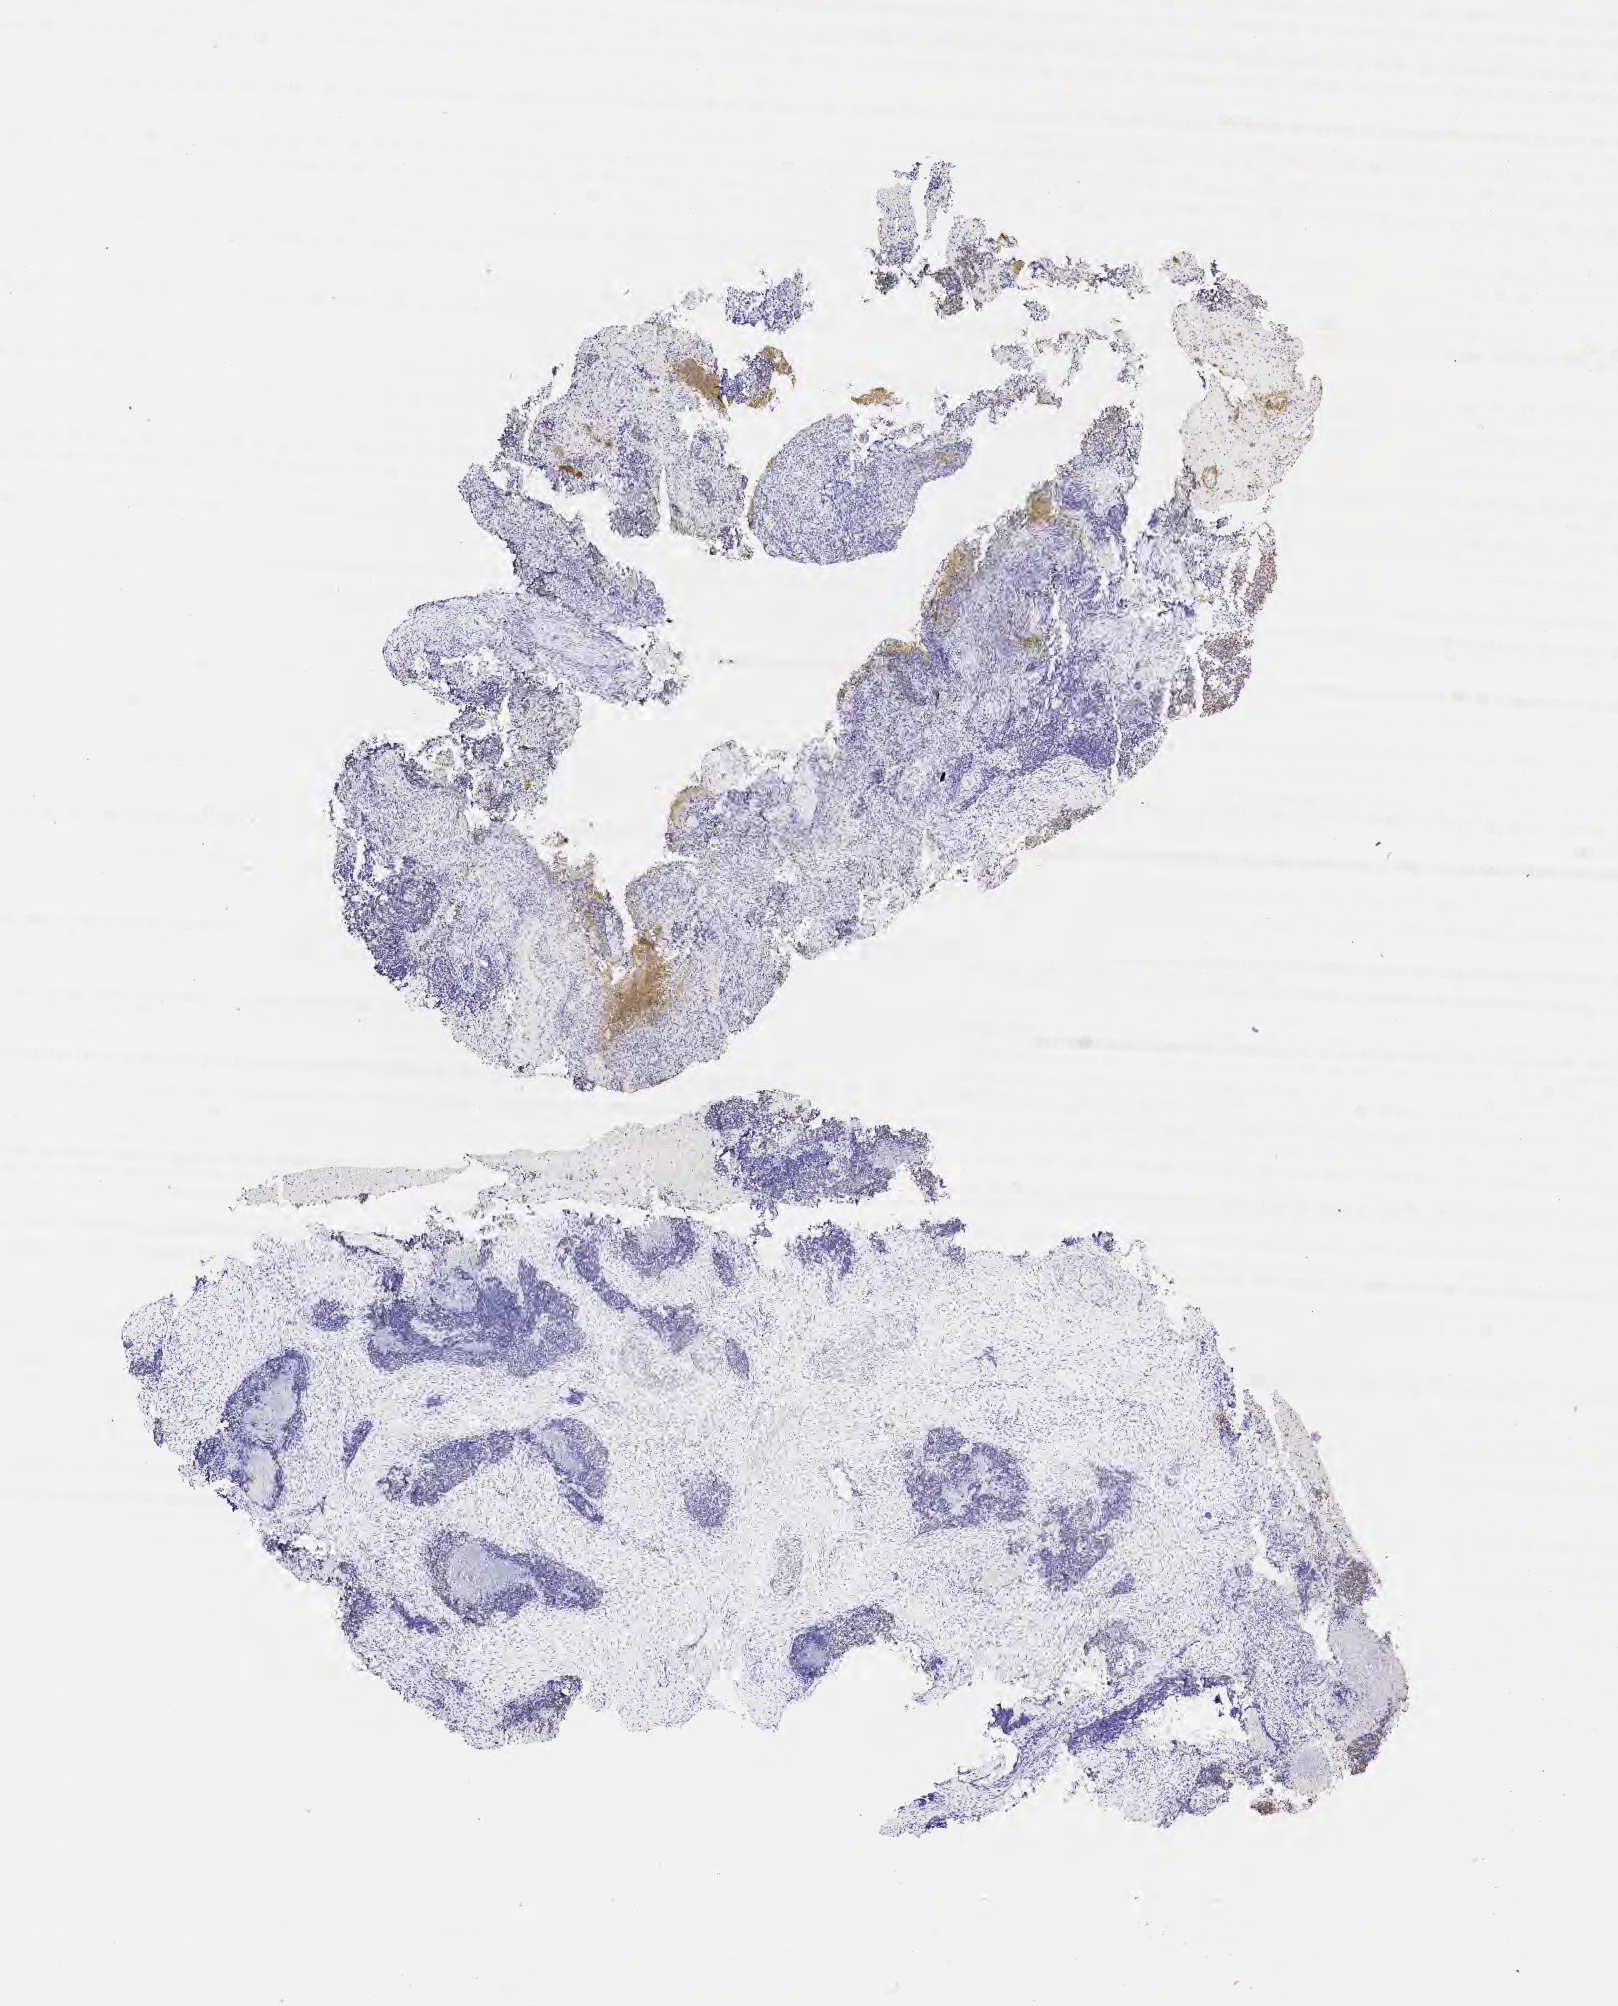
Immunohistochemistry (IHC) whole-slide image stained for synaptophysin — low-resolution overview of the scanned area, about 6.5 x 8.1 mm. Specimen: tumor tissue. Anatomic site: cervix. Patient: female, aged 47.
- histologic diagnosis: Squamous cell carcinoma, large cell, nonkeratinizing, NOS